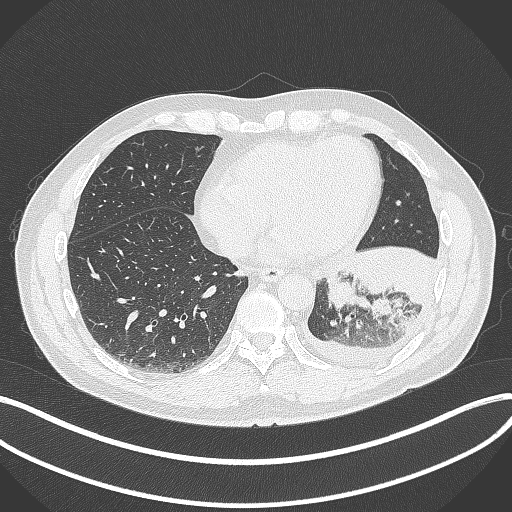
Chest CT, one axial slice; slice 112 of 342 in the series (ordered by position); reconstruction kernel B70f; 120 kVp; lung window (W 1500 / L -600 HU); 1 mm slice thickness; 512 × 512 image matrix, field of view 400 × 400 mm. Patient: male, 58 years. Case-level facts recorded for this patient, not image findings: clinical TNM (as recorded): T3 N1 M1b; histopathological grade: G3.
Annotated regions visible in this slice (bounding box drawn by a radiologist):
- lung tumour (recorded histology: small cell carcinoma): bounding box [x1, y1, x2, y2] px = [322, 264, 373, 312]